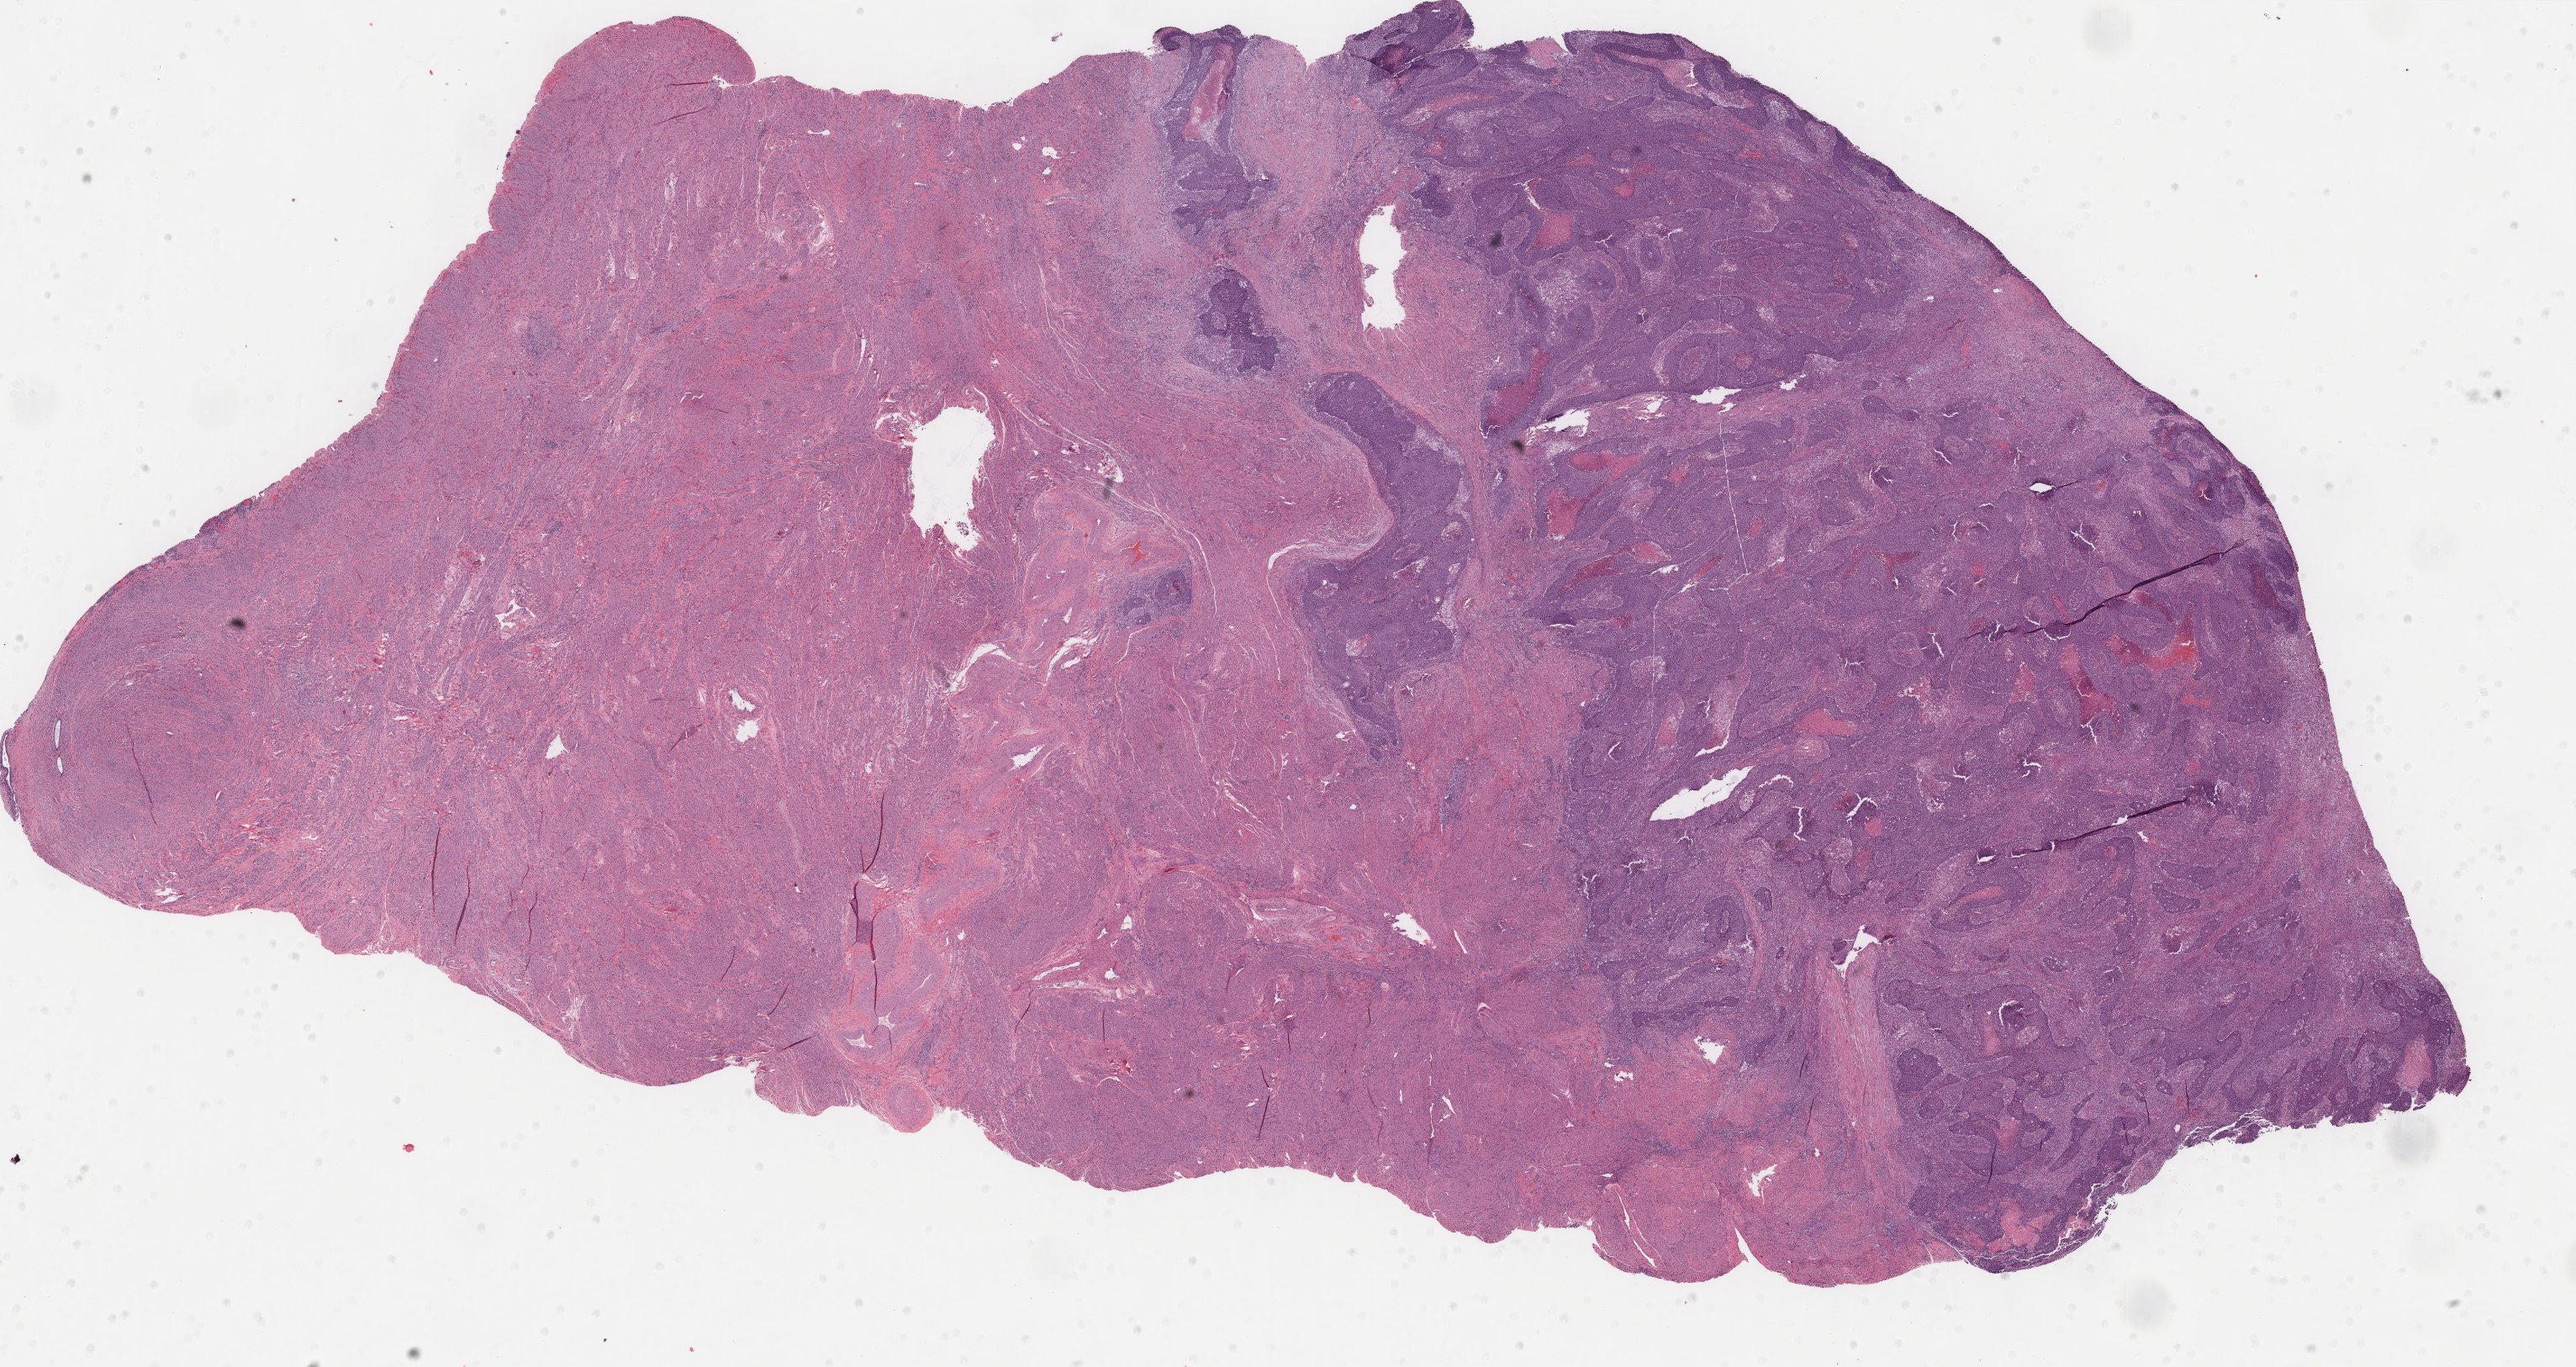
Whole-slide histology image, Hematoxylin and eosin (H&E) stained, a low-resolution overview of the entire scanned area, about 24.3 x 12.9 mm; formalin-fixed paraffin-embedded (FFPE) diagnostic section; uterus, primary tumour sample. Female, age 70 years at initial diagnosis. Histologic grade: G3 (poorly differentiated).
Histologic diagnosis: Endometrioid adenocarcinoma, NOS (endometrium). FIGO stage: IIIC. Lymph nodes positive (case pathology): 3 of 3 examined.